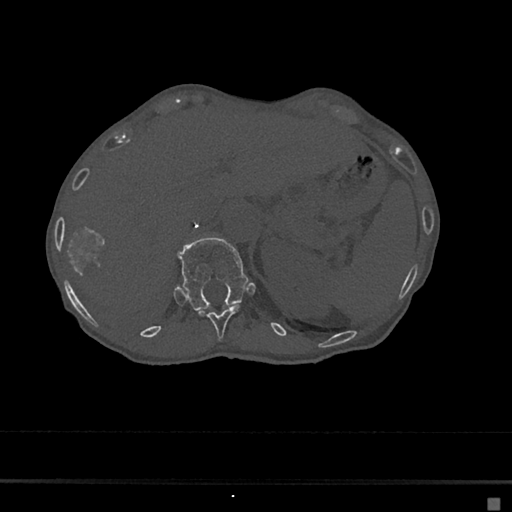
CT including the spine, one axial slice; slice 140 of 797 in the series (ordered by position); 120 kVp; bone window (W 1800 / L 400 HU); 0.5 mm slice thickness; 512 × 512 image matrix, field of view 360 × 360 mm. Female patient, age 68 years. Case-level facts recorded for this patient, not image findings: primary cancer: renal.
Outlined on this slice (semi-automatic segmentation, software-assisted and operator-edited):
- T11 vertebra: bounding box (x1, y1, x2, y2) in pixels: (198, 305, 242, 339)
- T12 vertebra: (178, 237, 249, 311)